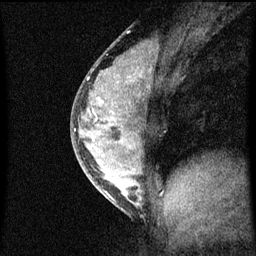
Breast MRI (dynamic contrast-enhanced), one sagittal slice. Position 30 of 60 along the scan axis. Dynamic contrast-enhanced series, image 2 of 3 at this slice position (ordered by acquisition). 1.5 T. TE 4.2 ms, TR 8 ms. 2 mm slice thickness. 256 × 256 image matrix, field of view 180 × 180 mm. Female patient, age 33 years.
Structures marked on this image (semi-automatically segmented with operator editing):
- analysis volume of interest (the breast-tissue region the enhancement analysis was run in; not a lesion): bounding box [x1, y1, x2, y2] px = [71, 56, 158, 215]
- tumour enhancement mask (voxels above the 70 % enhancement threshold inside the analysis volume of interest): [88, 74, 142, 205]